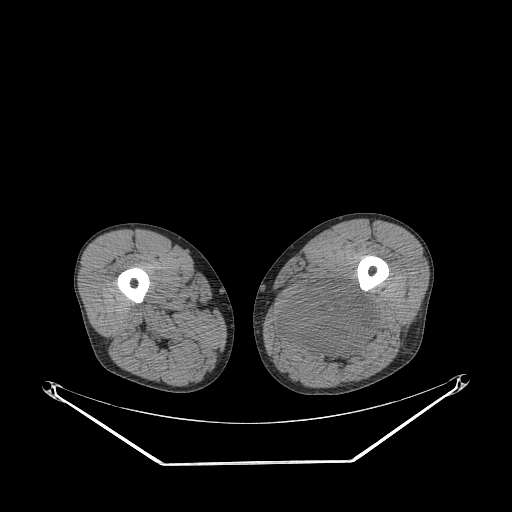
CT of an extremity soft-tissue mass (from a PET/CT study), one axial slice. Slice 242 of 267 in the series (ordered by position). Reconstruction kernel STANDARD. 140 kVp. Soft-tissue window (W 400 / L 40 HU). 3.75 mm slice thickness. 512 × 512 image matrix, field of view 500 × 500 mm. Male patient. Case-level facts recorded for this patient, not image findings: histological type: undifferentiated pleomorphic liposarcoma; grade: high; site of the primary tumour: left thigh.
Annotated regions visible in this slice (expert contour drawn on MRI and transferred to this co-registered scan by the dataset authors):
- gross tumour volume including surrounding oedema: box from (x=276, y=285) to (x=375, y=362) px
- gross tumour volume (mass): (x=281, y=285)–(x=375, y=353)